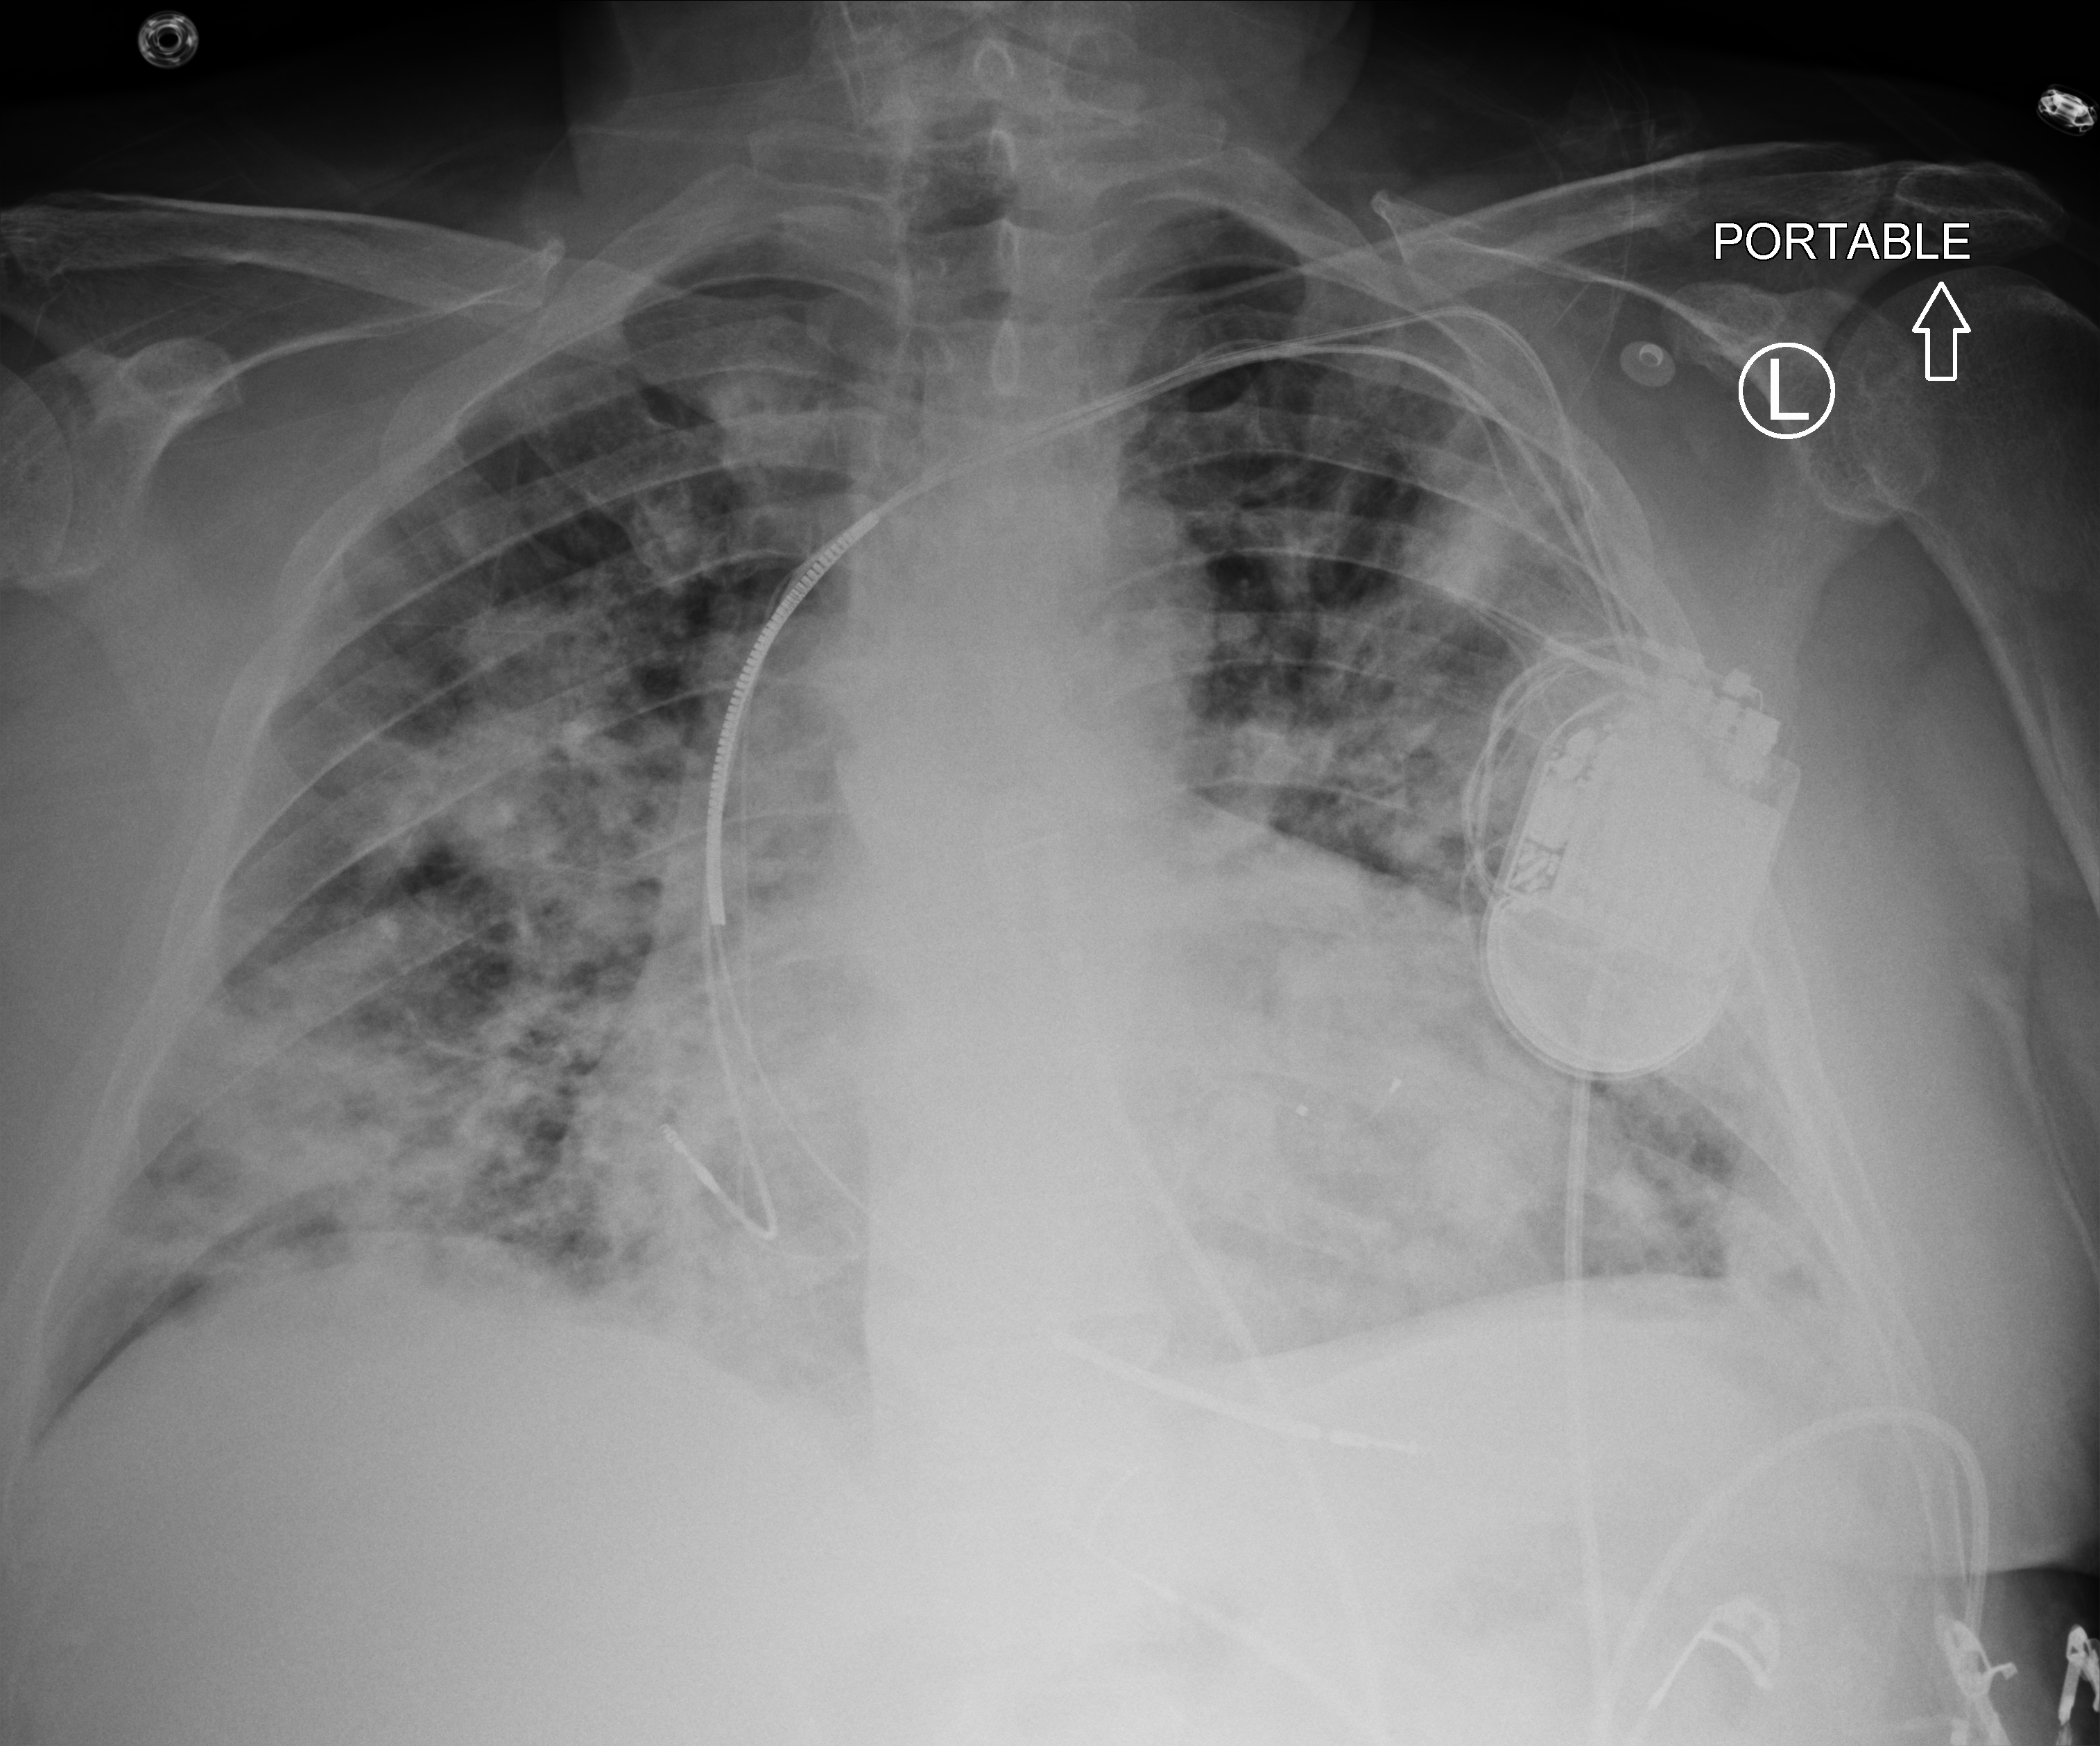
Portable chest radiograph; anteroposterior (AP) projection. Patient hospitalised with COVID-19; male, aged 60–74 years.
From the hospital-stay record, not from the radiograph (when in the stay this image was taken is not recorded): admitted to intensive care during this hospital stay: no.